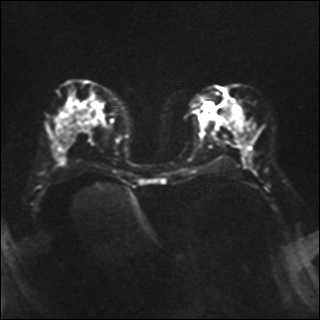
Breast MRI, one axial slice; position 15 of 35 along the scan axis; diffusion-weighted series; image 2 of 4 stored at this slice position (different b-values; order by instance number); 1.5 T; 4 mm slice thickness; 320 × 320 image matrix. Female patient.
Annotated regions visible in this slice (manually delineated by an expert):
- tumour on diffusion-weighted imaging: bounding box (x1, y1, x2, y2) in pixels: (212, 100, 232, 122)